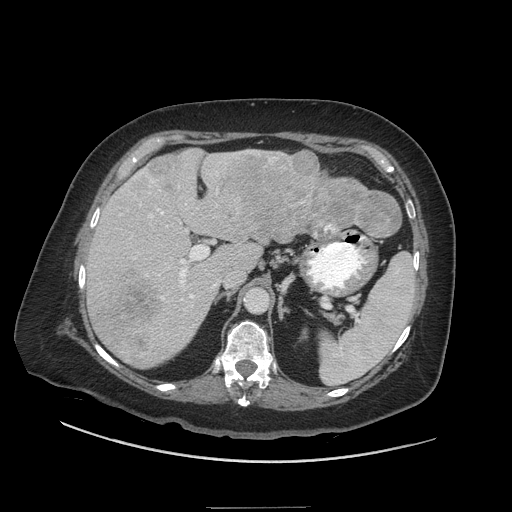
Contrast-enhanced abdominal CT (liver protocol), one axial slice. Reconstruction kernel STANDARD. 140 kVp. Soft-tissue window (W 400 / L 40 HU). 2.5 mm slice thickness. 512 × 512 image matrix, field of view 440 × 440 mm. From the clinical record (not read from this slice): diagnosis: hepatocellular carcinoma (patient treated with transarterial chemoembolisation; whether this scan precedes or follows treatment is not stated here); TNM stage (as recorded): Stage-II; Child-Pugh class: A; tumour differentiation: moderately differentiated; tumour nodularity: multinodular.
Annotated regions visible in this slice (semi-automatic segmentation, software-assisted and operator-edited):
- liver parenchyma outside the tumour (the mass and vessels are separate outlines, so this box may not span the whole liver): box from (x=86, y=148) to (x=357, y=368) px
- mass: (x=101, y=150)–(x=402, y=352)
- liver vessels: (x=119, y=150)–(x=257, y=356)